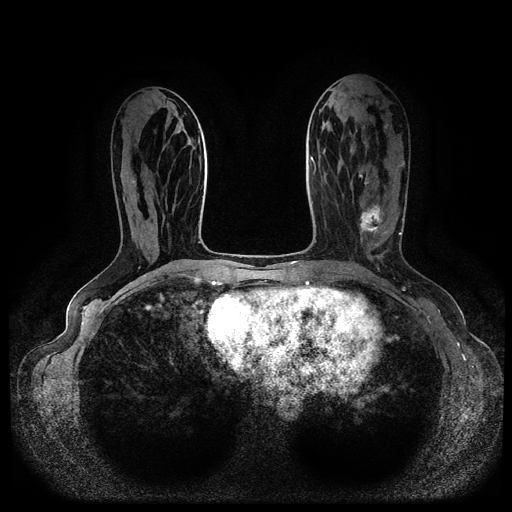
Breast MRI (dynamic contrast-enhanced, multi-phase), one axial slice; slice 43 of 116 in the series (ordered by position); dynamic contrast-enhanced series, time point 2 of 5 at this slice position (early post-contrast); 1.5 T; TE 2.6 ms, TR 5.3 ms; 2 mm slice thickness; 512 × 512 image matrix, field of view 350 × 350 mm. Patient: female, 45 years.
Annotated regions visible in this slice (semi-automatic segmentation, software-assisted and operator-edited):
- breast lesion (labelled 'tumour' in the annotation; benign lesions carry a separate 'benign' label): bounding box [x1, y1, x2, y2] px = [359, 204, 386, 240]